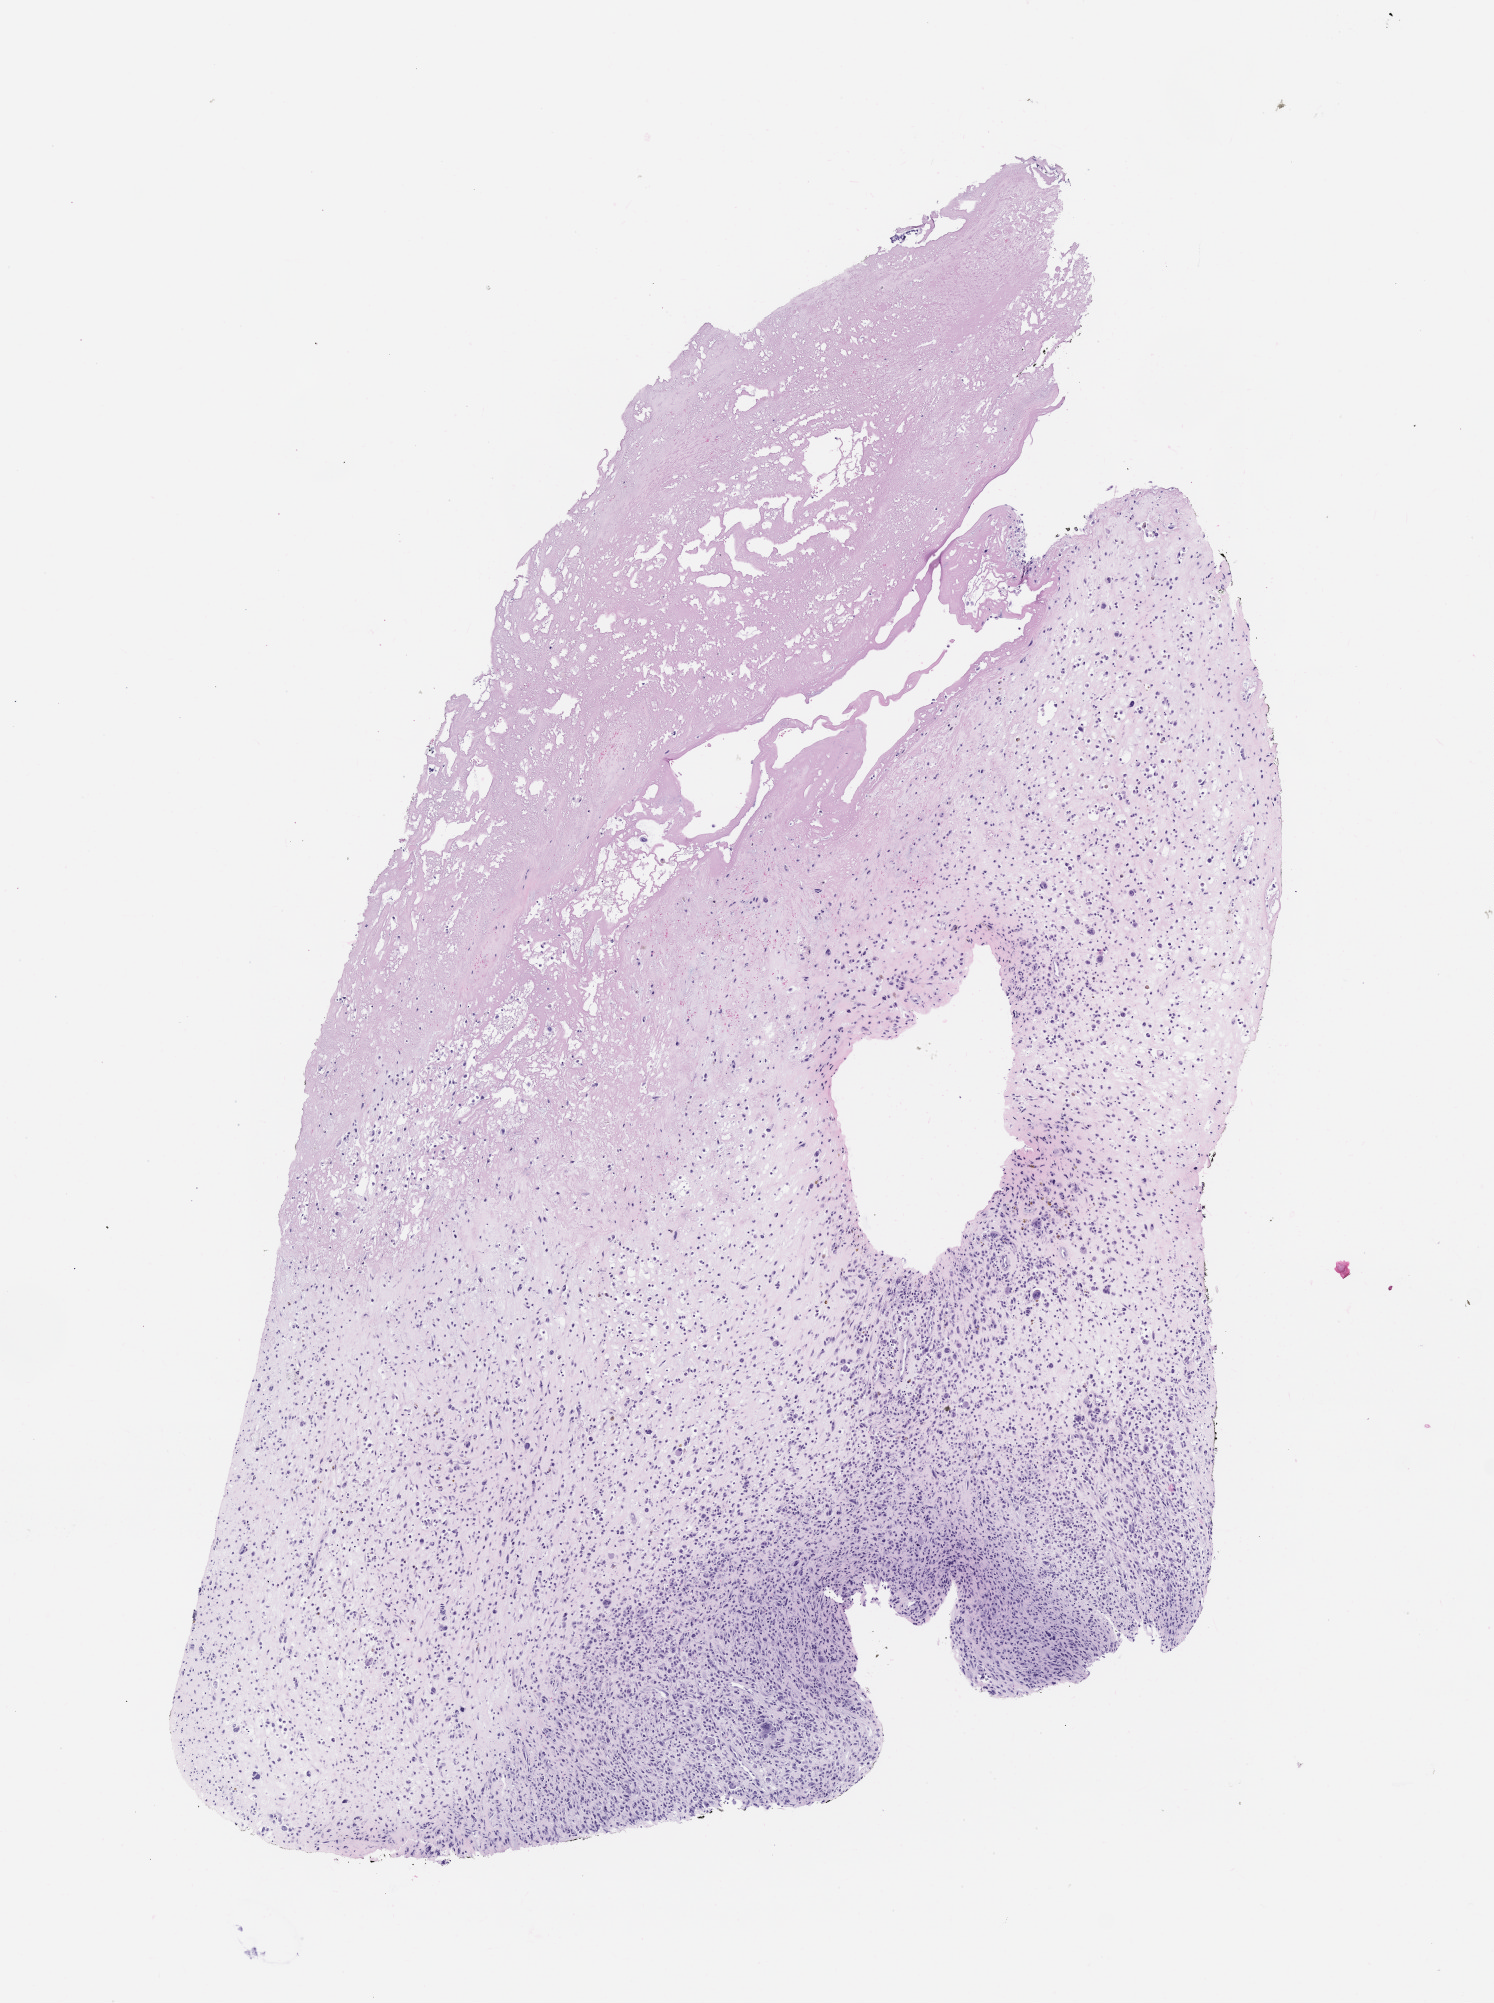
Whole-slide image, H&E stain of the patient's (originator) tumor tissue, a low-resolution overview of the entire scanned area, about 6.0 x 8.1 mm, formalin-fixed paraffin-embedded section, originating tumor site category: bone. Patient: female, age 55 years.
Diagnosis: Osteosarcoma.